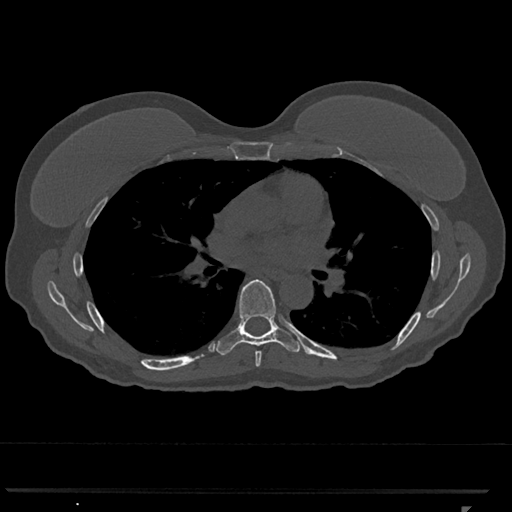
CT including the spine, one axial slice; slice 722 of 793 in the series (ordered by position); bone window (W 1800 / L 400 HU); 512 × 512 image matrix, field of view 380 × 380 mm. Patient: female, 62 years. Case-level facts recorded for this patient, not image findings: primary cancer: renal.
Structures marked on this image (semi-automatic segmentation, software-assisted and operator-edited):
- T6 vertebra: bounding box <255,351,262,367> (left, top, right, bottom; pixels)
- T7 vertebra: <216,279,302,356>